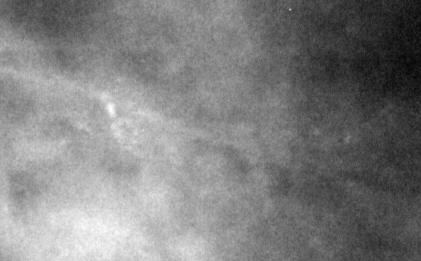
Crop from a digitized film mammogram around one marked abnormality; right breast; MLO view; BI-RADS breast density category 3 (scale 1–4).
Finding: calcifications, morphology pleomorphic, distribution linear; BI-RADS assessment category 4; pathology (as recorded): malignant.